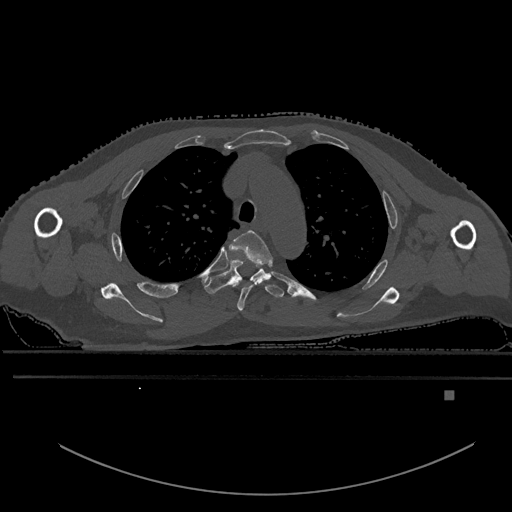
CT including the spine, one axial slice; position 426 of 969 along the scan axis; bone window (W 1800 / L 400 HU); 0.5 mm slice thickness; 512 × 512 image matrix, field of view 456 × 456 mm. Patient: male, 82 years. From the clinical record (not read from this slice): primary cancer: prostate; vertebrae with lytic lesions (as recorded): T11, T9, T8, T2.
Outlined on this slice (semi-automatic segmentation, software-assisted and operator-edited):
- T3 vertebra: bounding box (x1, y1, x2, y2) in pixels: (229, 230, 273, 311)
- T4 vertebra: (203, 260, 284, 298)